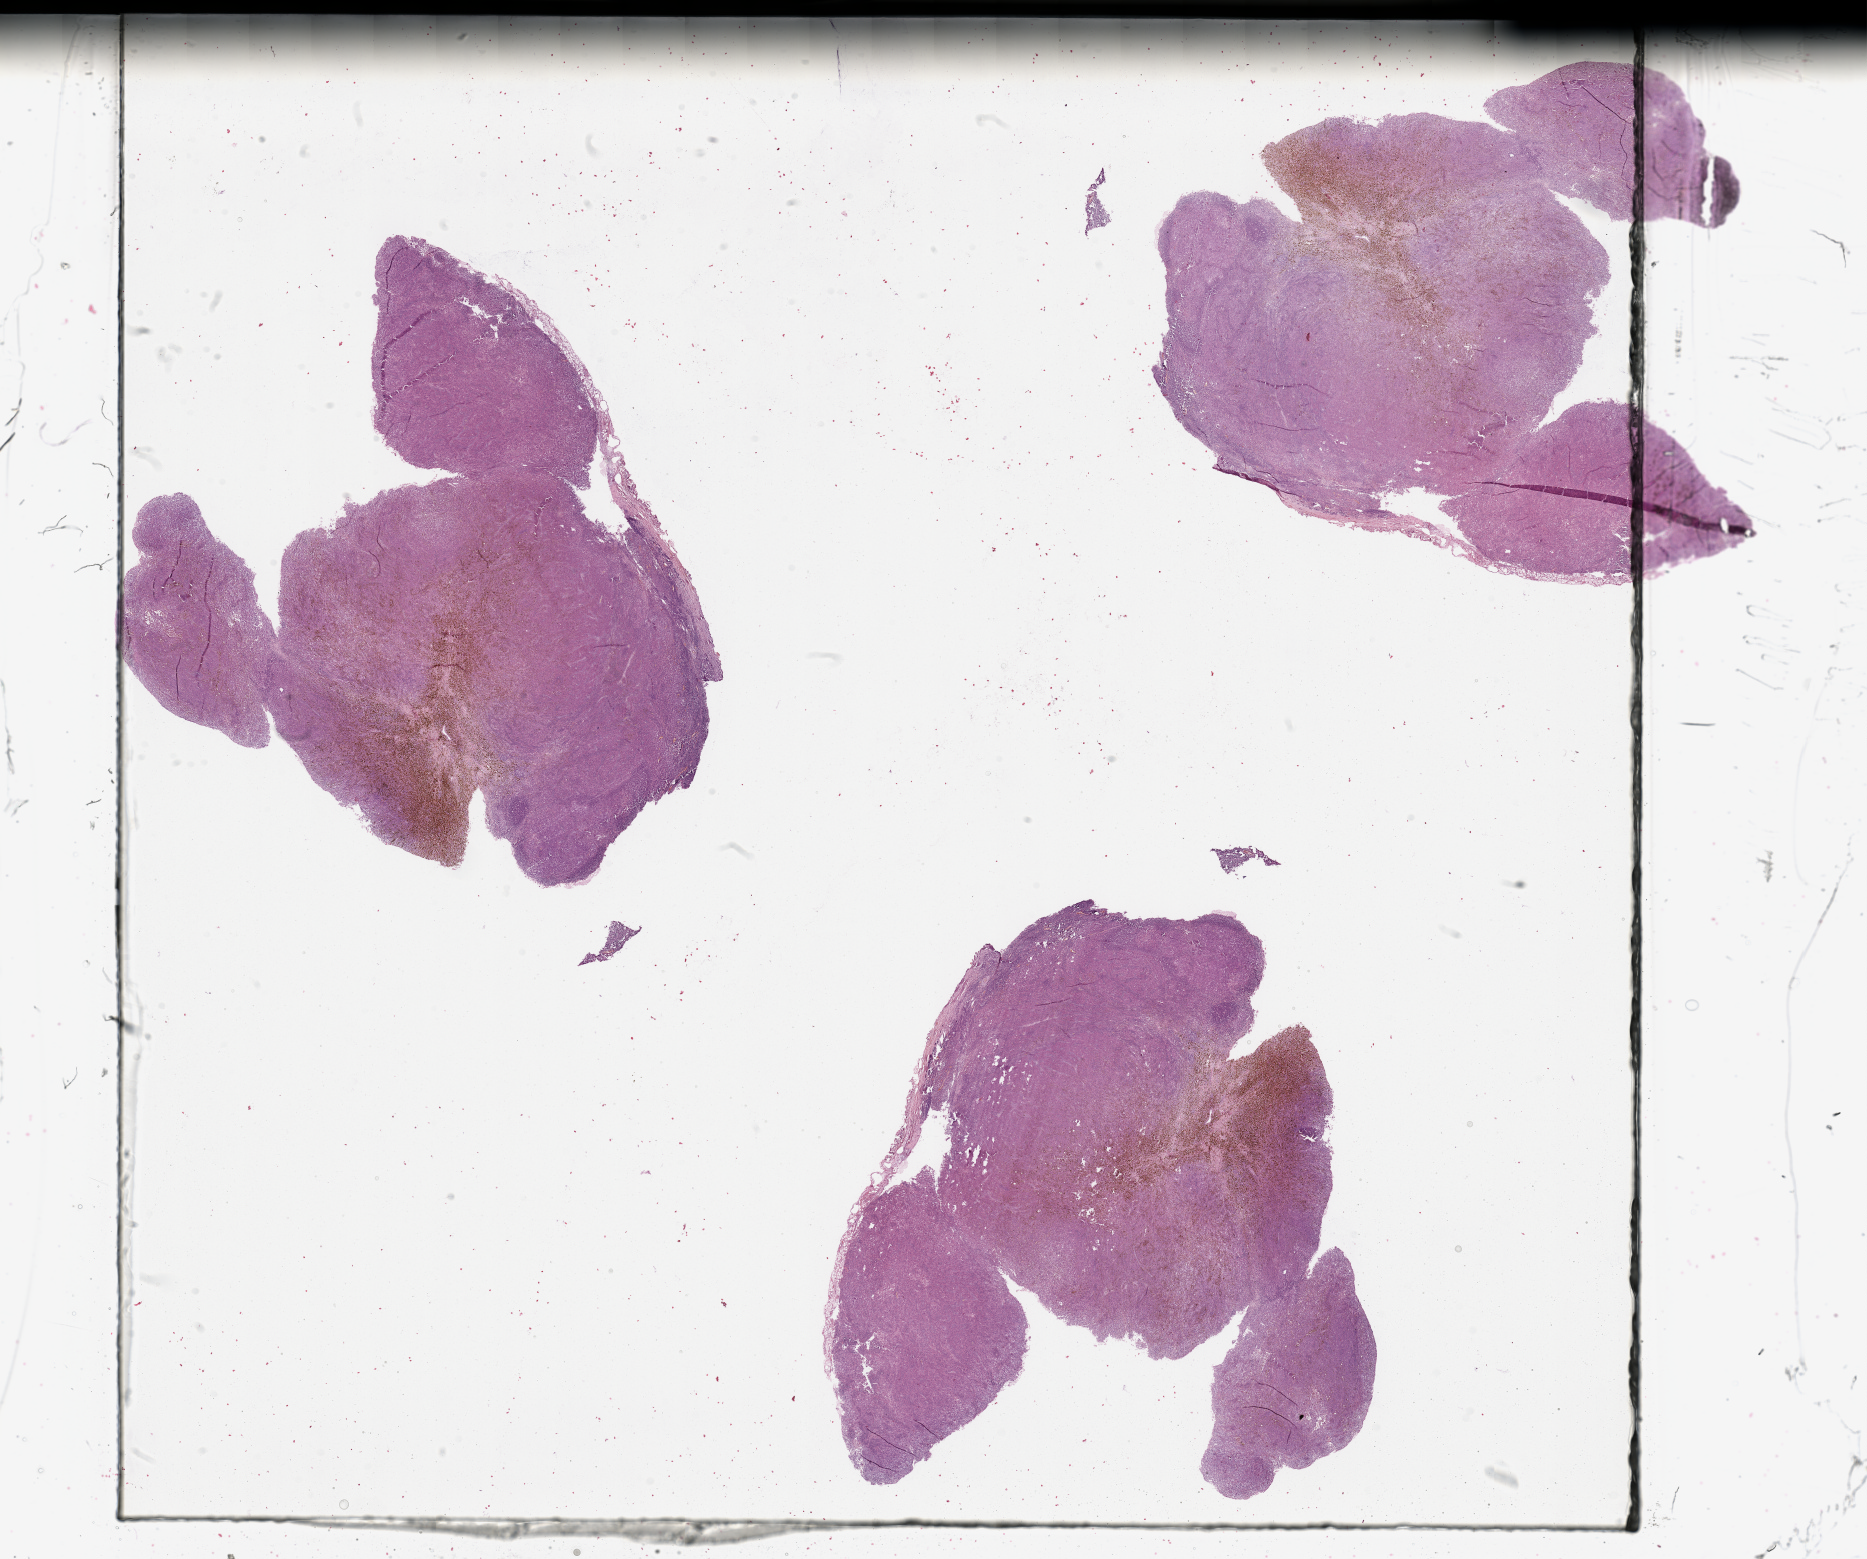
Whole-slide histology image, Hematoxylin and eosin (H&E) stained, shown as a low-resolution overview of the whole scanned area (about 29.5 x 24.7 mm), melanoma tumour tissue; sampled site not recorded. Patient: male, age 62 years.
Histologic diagnosis: Malignant melanoma, NOS.